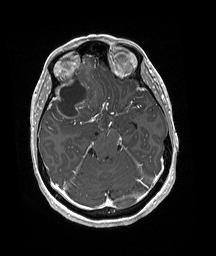
Brain MRI from a brain-tumour surgery series, one axial slice; position 120 of 192 along the scan axis; T1-weighted post-contrast; 1 mm slice thickness; 216 × 256 image matrix, field of view 211 × 250 mm. Case-level facts recorded for this patient, not image findings: histopathology: Oligodendroglioma; WHO grade: 3; IDH mutation: yes.
Annotated regions visible in this slice (expert manual segmentation):
- tumour: bounding box <50,73,96,119> (left, top, right, bottom; pixels)